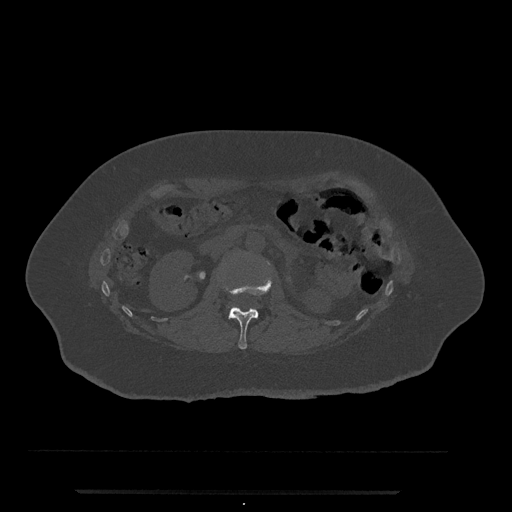
CT including the spine, one axial slice. Slice 82 of 797 in the series (ordered by position). Bone window (W 1800 / L 400 HU). 0.5 mm slice thickness. 512 × 512 image matrix. Female patient, age 51 years. From the clinical record (not read from this slice): primary cancer: neuro; vertebrae with lytic lesions (as recorded): T8.
Annotated regions visible in this slice (semi-automatically segmented with operator editing):
- L1 vertebra: box from (x=223, y=277) to (x=273, y=350) px
- L2 vertebra: (x=229, y=306)–(x=238, y=311)